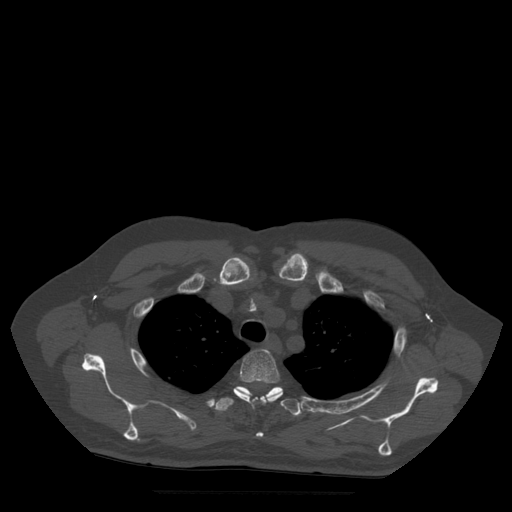
CT including the spine, one axial slice. Position 403 of 522 along the scan axis. Bone window (W 1800 / L 400 HU). 1.25 mm slice thickness. 512 × 512 image matrix. Patient age 72 years. From the clinical record (not read from this slice): primary cancer: prostate.
Annotated regions visible in this slice (semi-automatically segmented with operator editing):
- T3 vertebra: box from (x=234, y=349) to (x=283, y=438) px
- T4 vertebra: (x=215, y=387)–(x=302, y=416)